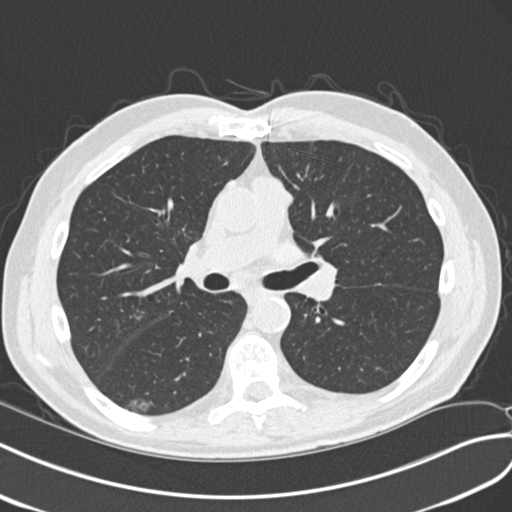
Low-dose screening chest CT, axial slice, second screening round (one year after baseline), lung window (W 1500 / L -600 HU), 2 mm slice thickness, standard (soft-tissue) reconstruction kernel (B30f). Male participant, aged 68 years at enrolment. Current smoker at enrolment.
Lesion marked by an expert reader, bounding box (x1, y1, x2, y2) in pixels: (115, 387, 164, 423). The screening reader recorded 4 non-calcified nodules or masses ≥4 mm on this exam (right upper lobe, left upper lobe, right upper lobe, right lower lobe); which of them this box marks is not recorded. Later outcome: lung cancer diagnosed 653 days after this screen — non-small cell carcinoma, right lower lobe, poorly differentiated (G3), stage IA (AJCC 6th edition), 23 mm at pathology.